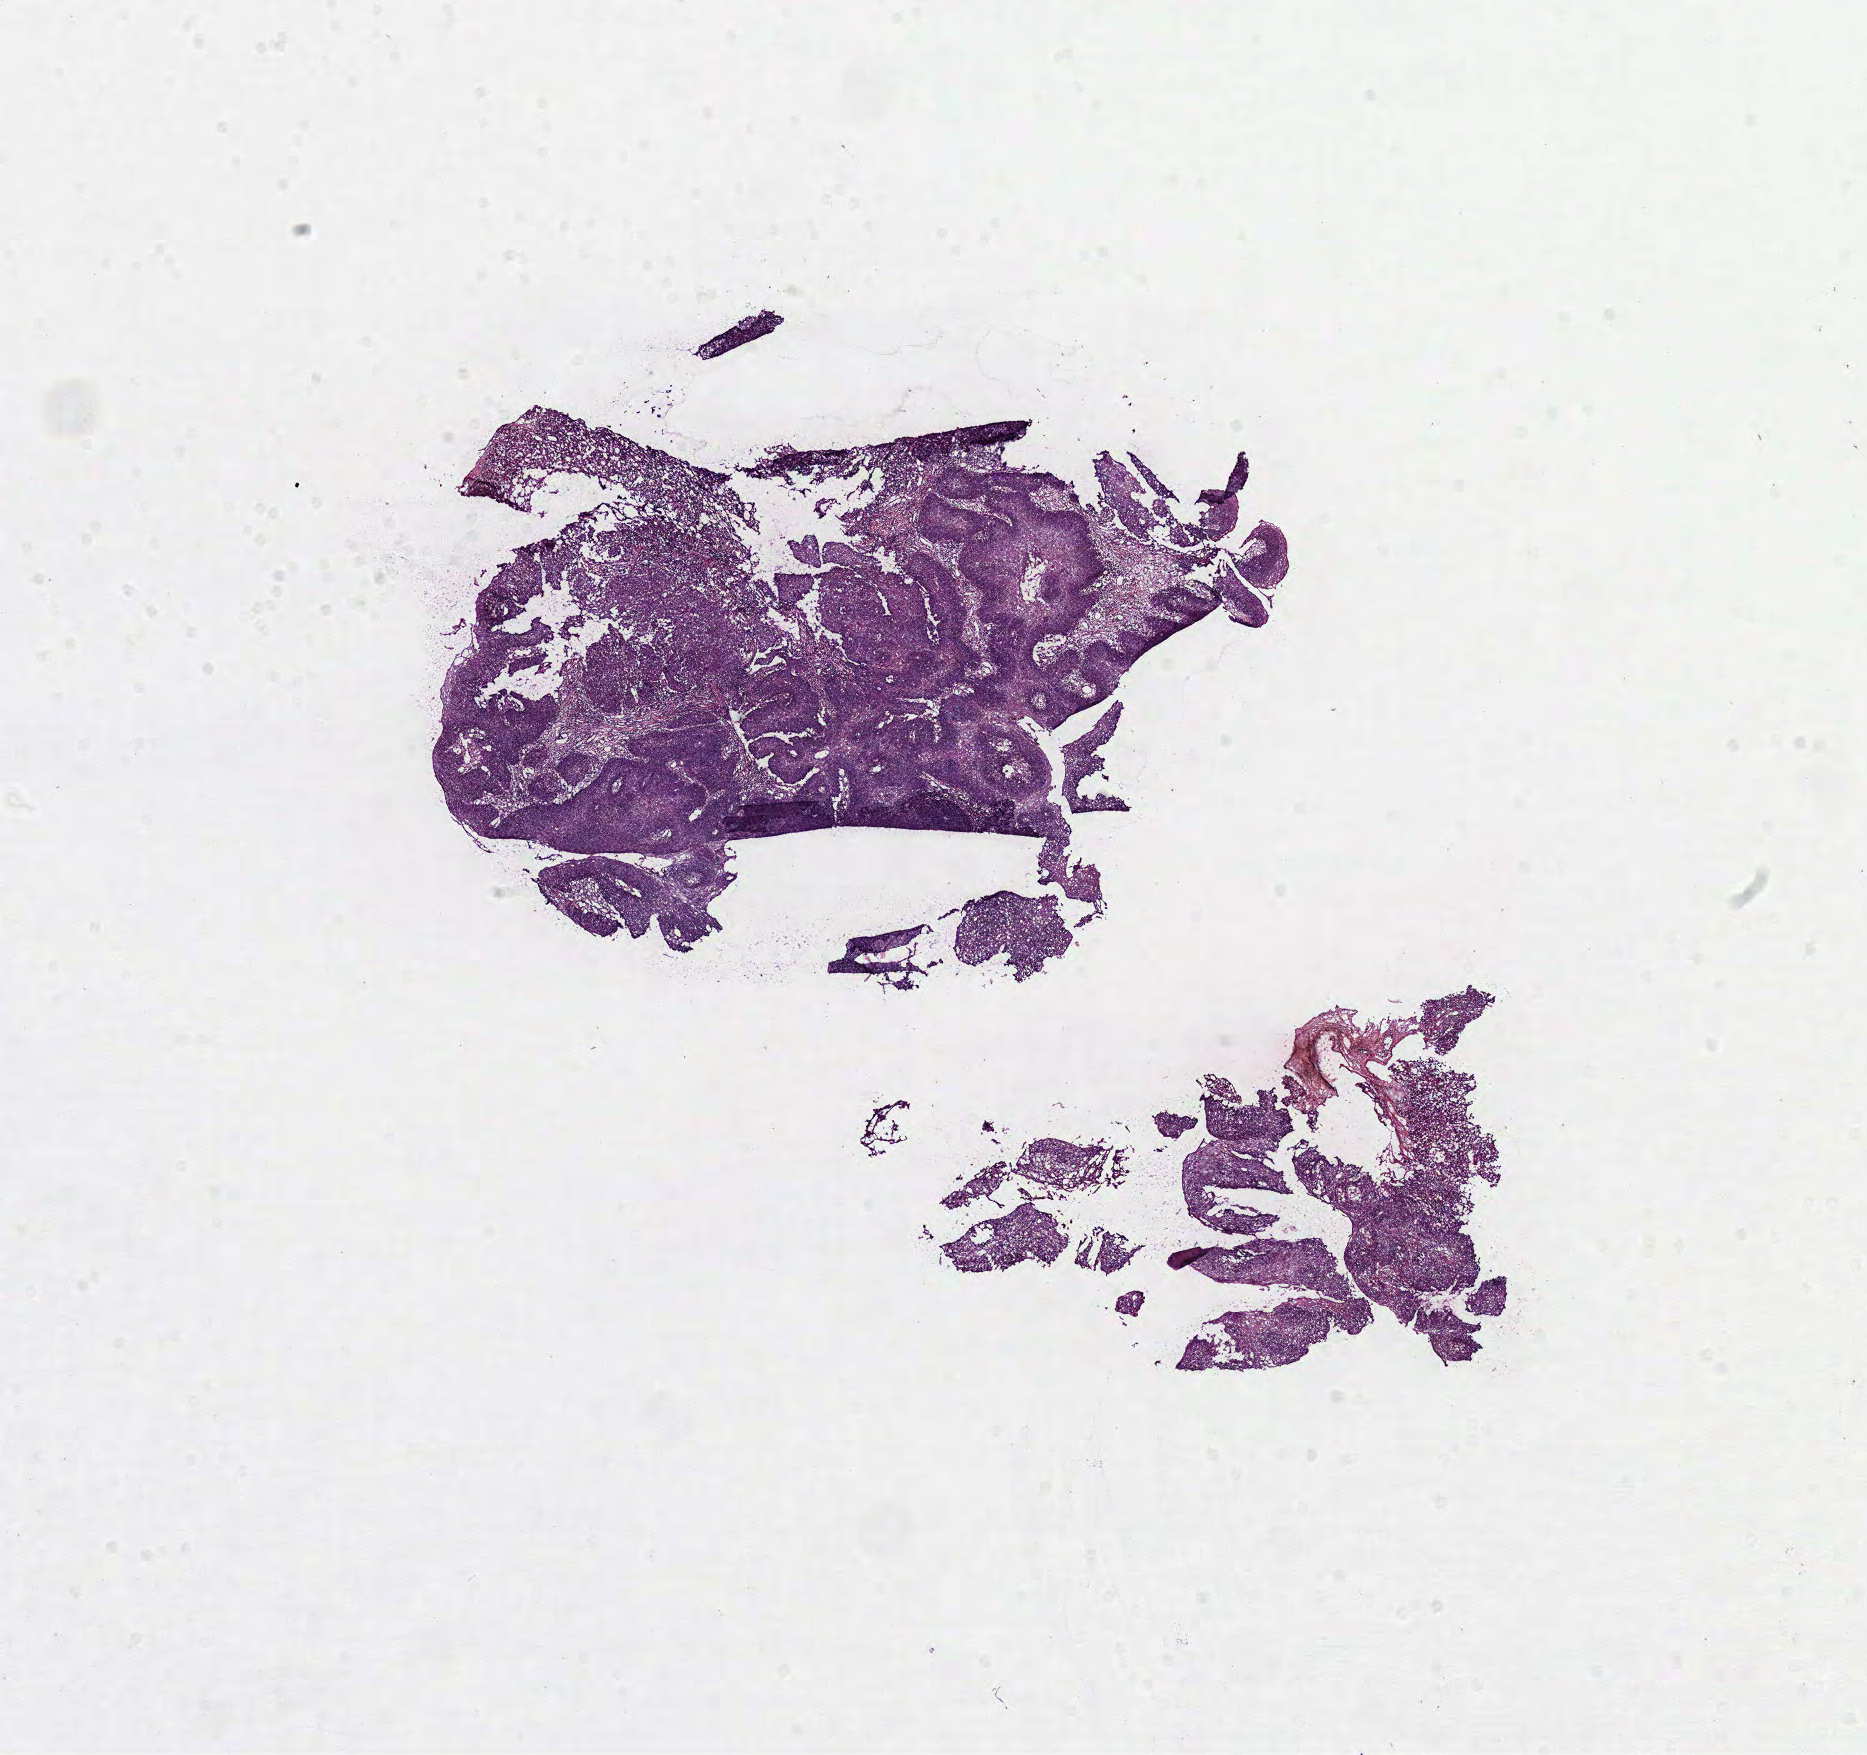
Whole-slide histology image, H&E-stained — a low-resolution overview of the entire scanned area, about 14.7 x 13.8 mm; formalin-fixed paraffin-embedded (FFPE) diagnostic section; head and neck, primary tumour sample. Female, age 58 years at initial diagnosis. Histologic grade: G3 (poorly differentiated).
AJCC pathologic stage: II. Histologic diagnosis: Squamous cell carcinoma, NOS (floor of mouth, NOS).